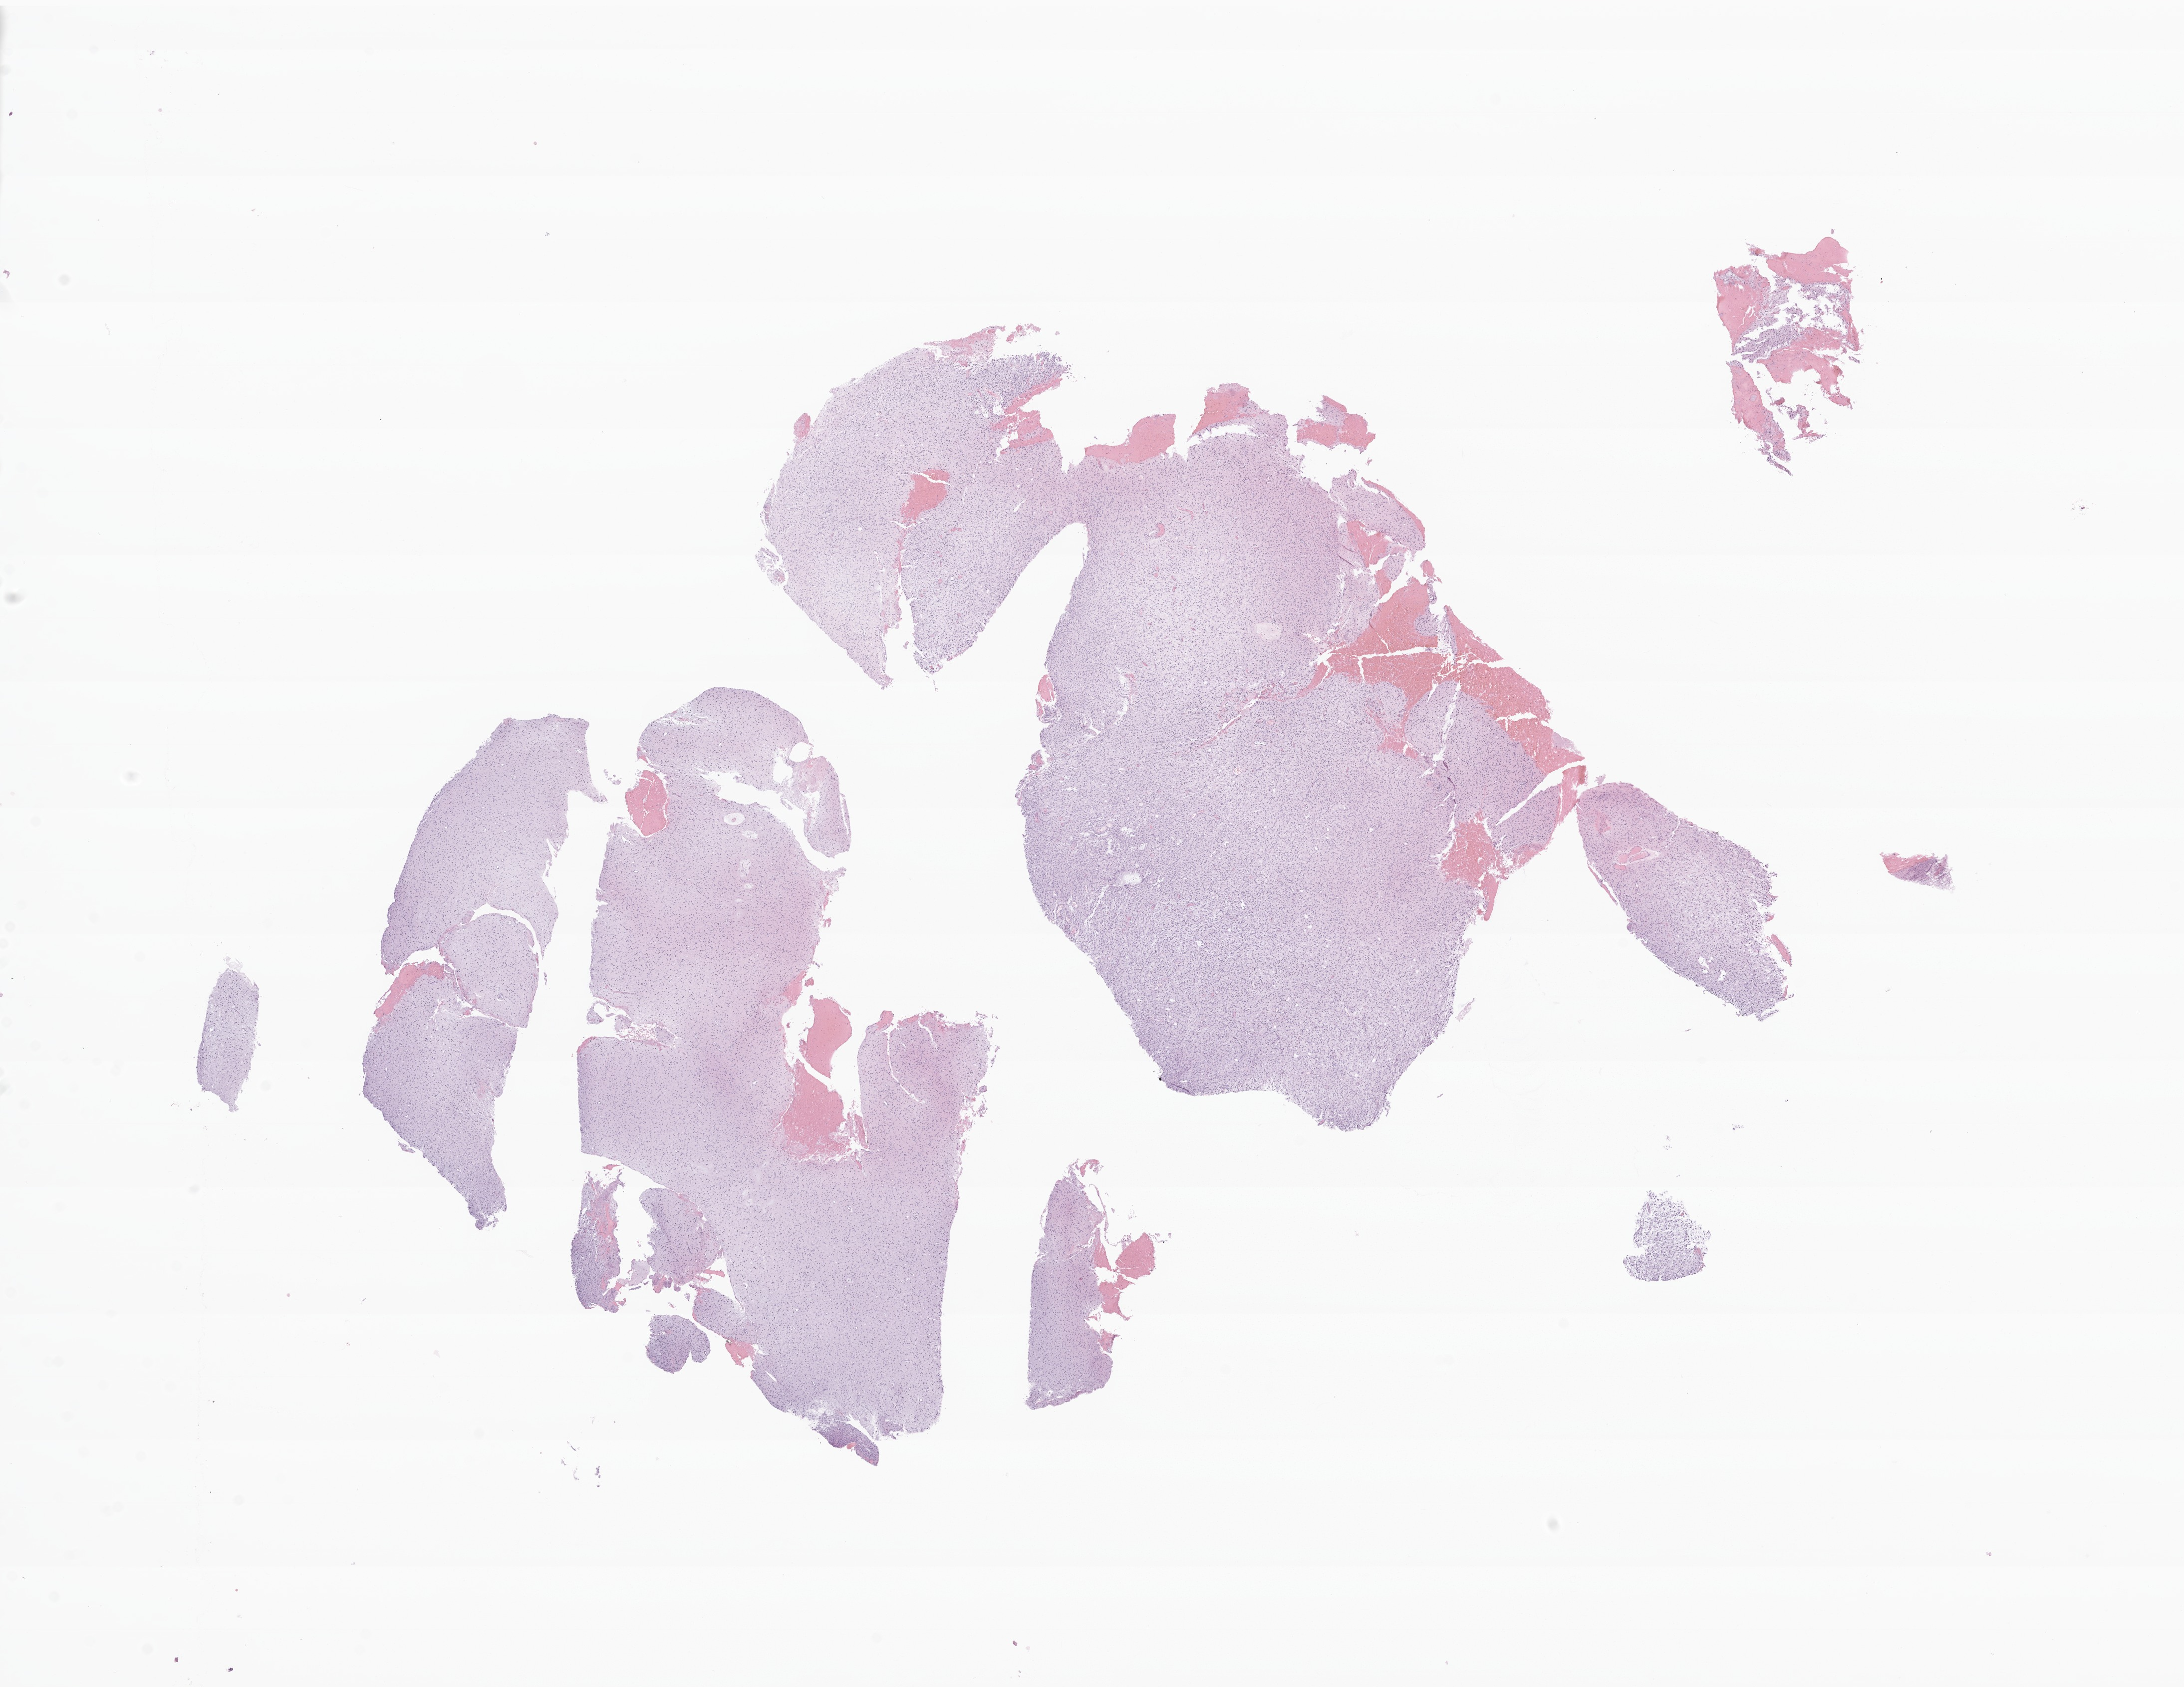
H&E whole-slide image of tumor tissue from the brain, shown as a low-resolution overview of the whole scanned area (about 18.4 x 14.2 mm); formalin-fixed, paraffin-embedded (FFPE) tissue. Patient: female, age 217 months (18 years 1 month).
* diagnosis: Astrocytoma, anaplastic, NOS